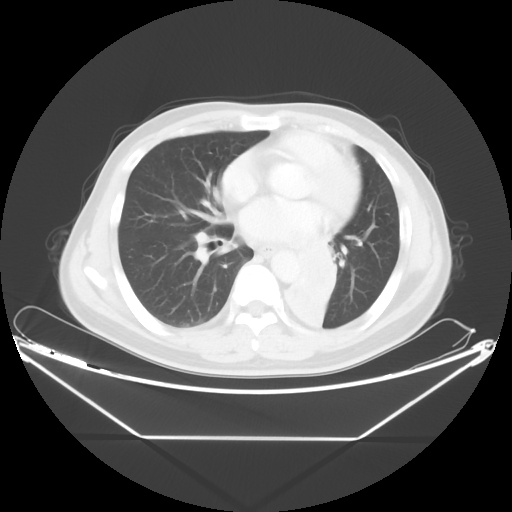
Chest CT, one axial slice. Slice 21 of 48 in the series (ordered by position). Reconstruction kernel STANDARD. 120 kVp. Lung window (W 1500 / L -600 HU). 512 × 512 image matrix, field of view 438 × 438 mm. Male patient, age 58 years. From the clinical record (not read from this slice): clinical TNM (as recorded): T3 N3 M0.
Structures marked on this image (bounding box drawn by a radiologist):
- lung tumour (recorded histology: squamous cell carcinoma): box from (x=278, y=228) to (x=345, y=342) px